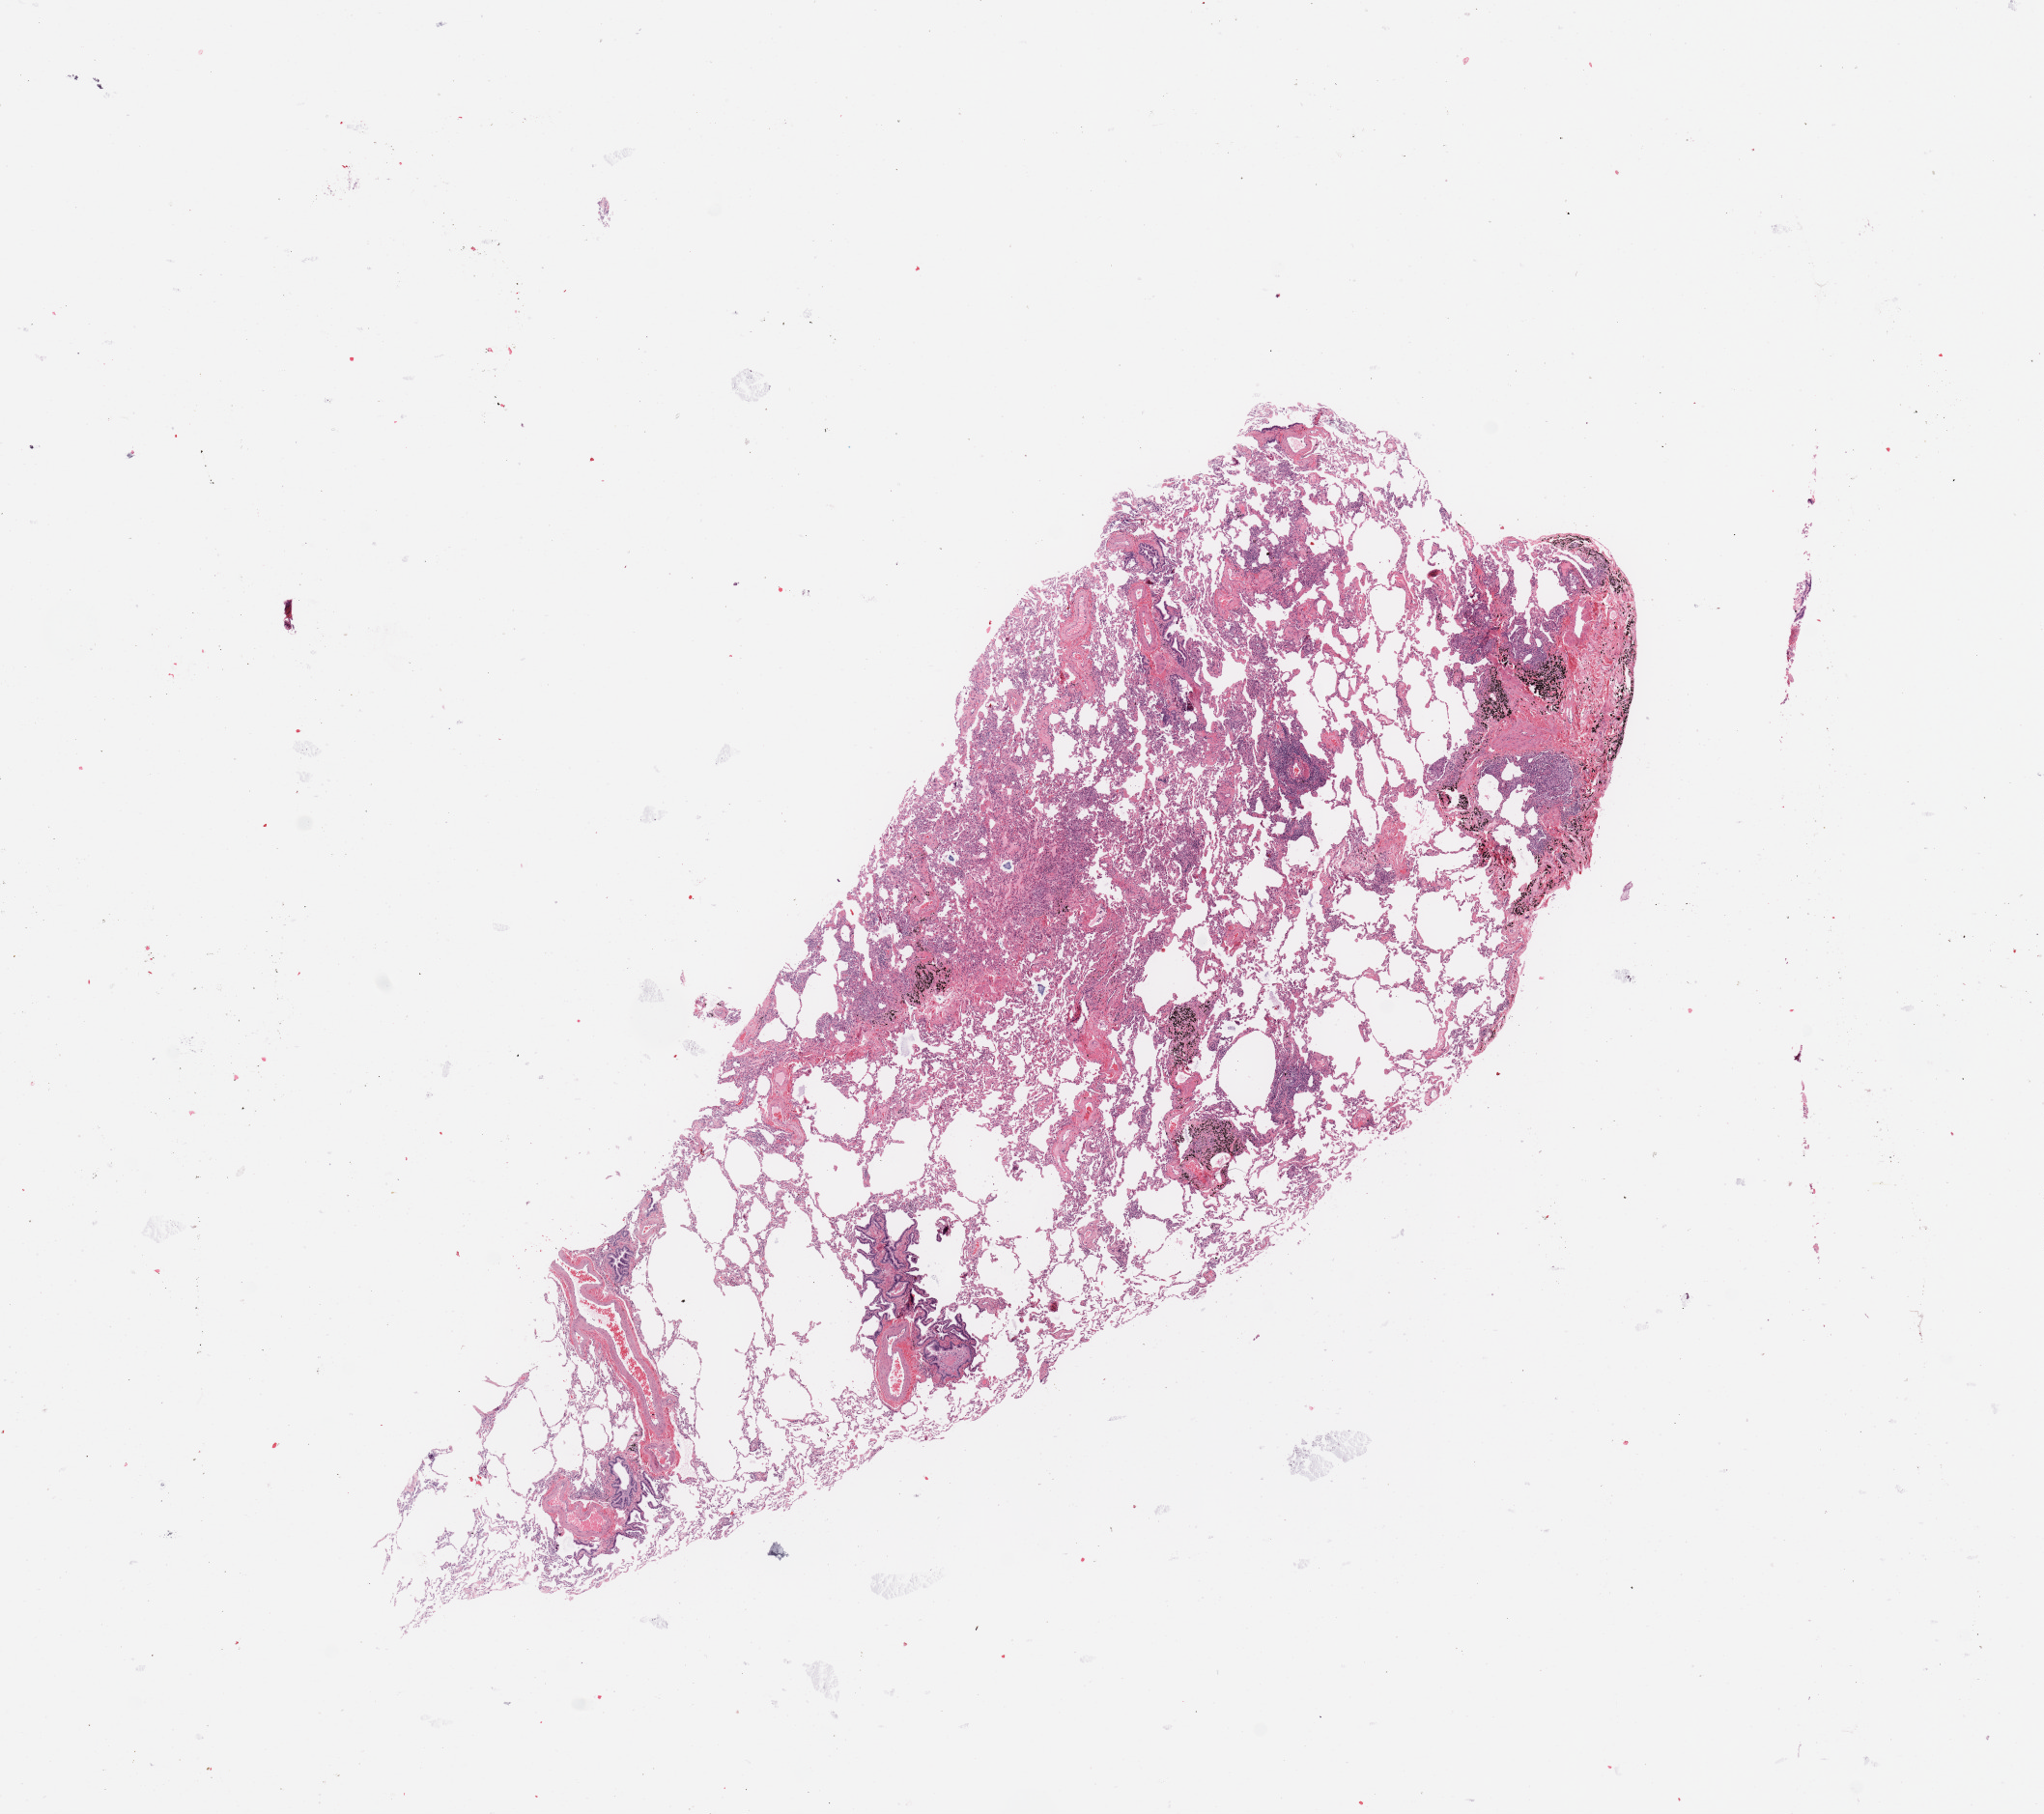
Hematoxylin and eosin (H&E) stained whole-slide image, low-resolution overview of the scanned area, about 16.7 x 14.9 mm (from a 20x scan); normal (non-tumour) tissue sample, sampled site: lung. Patient: male, age 68 years.
This section: normal (non-tumour) tissue from the same patient. Patient diagnosis: Adenocarcinoma, NOS.